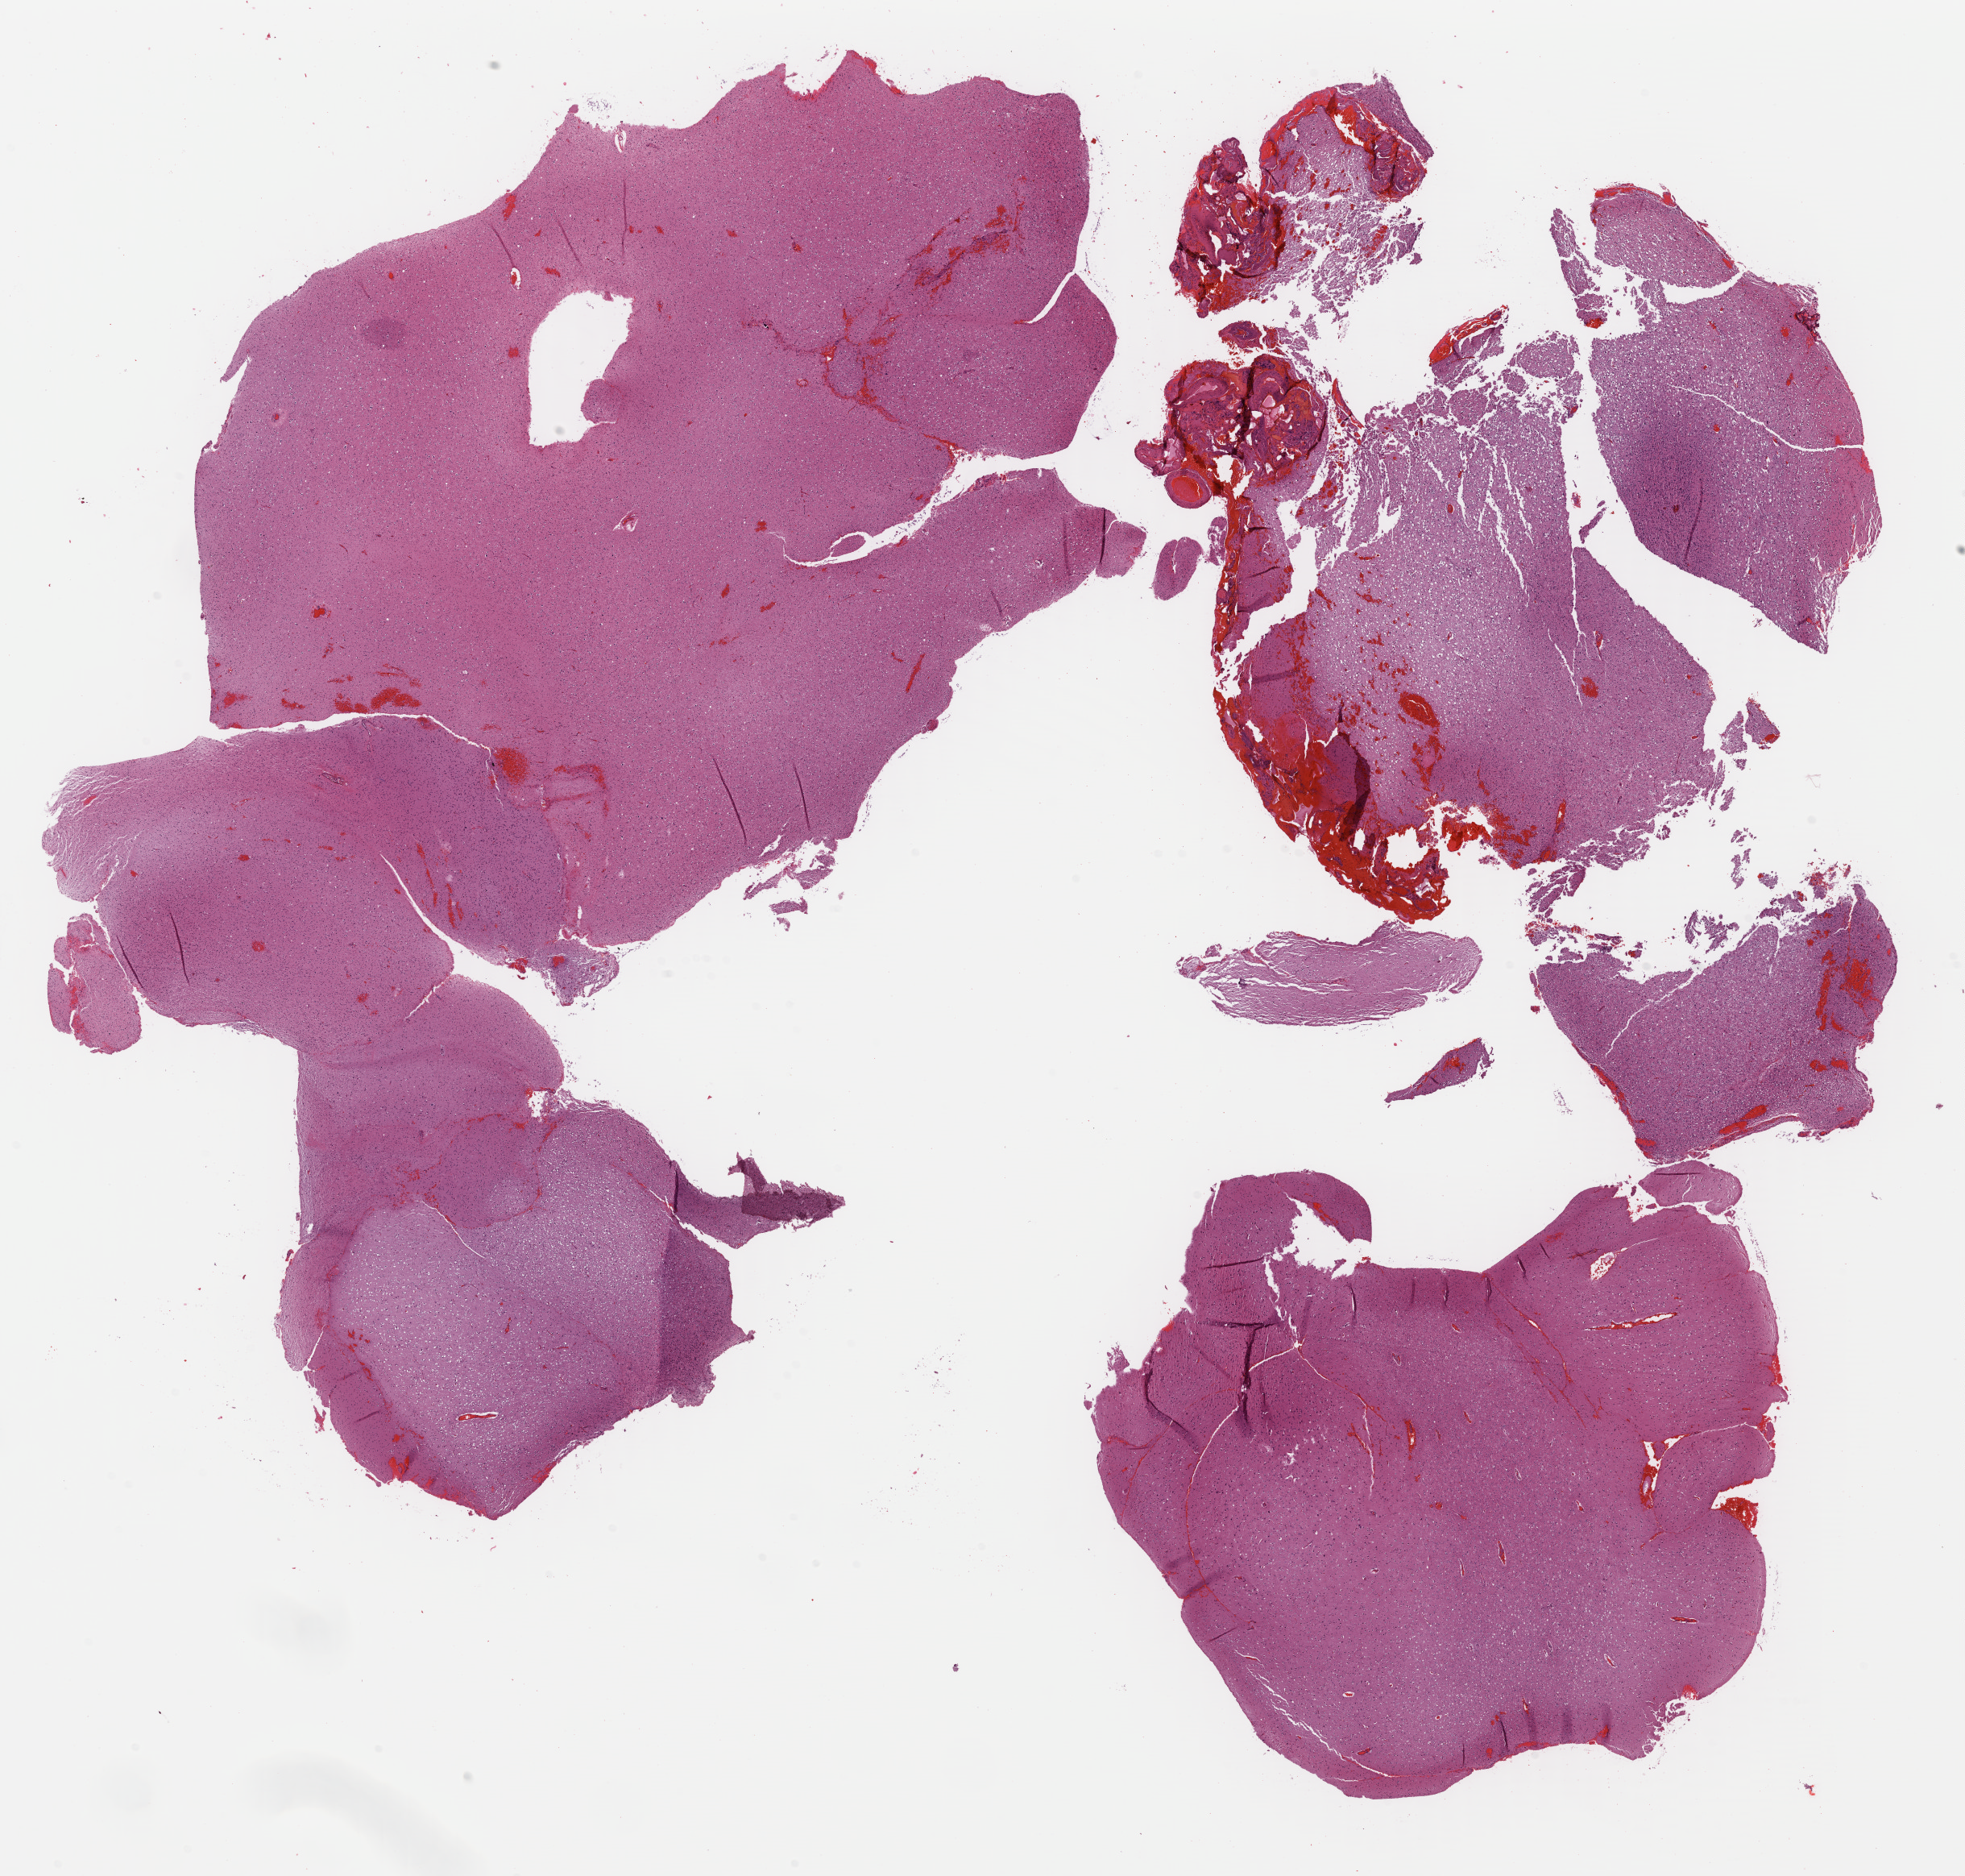
Whole-slide histology image, Hematoxylin and eosin (H&E) stained, low-resolution overview of the scanned area, about 19.2 x 18.3 mm, FFPE section, sample: primary tumour, brain. Male, age 44 years at initial diagnosis. Histologic grade: G3 (poorly differentiated).
• pathologic diagnosis: Astrocytoma, anaplastic
• laterality: right